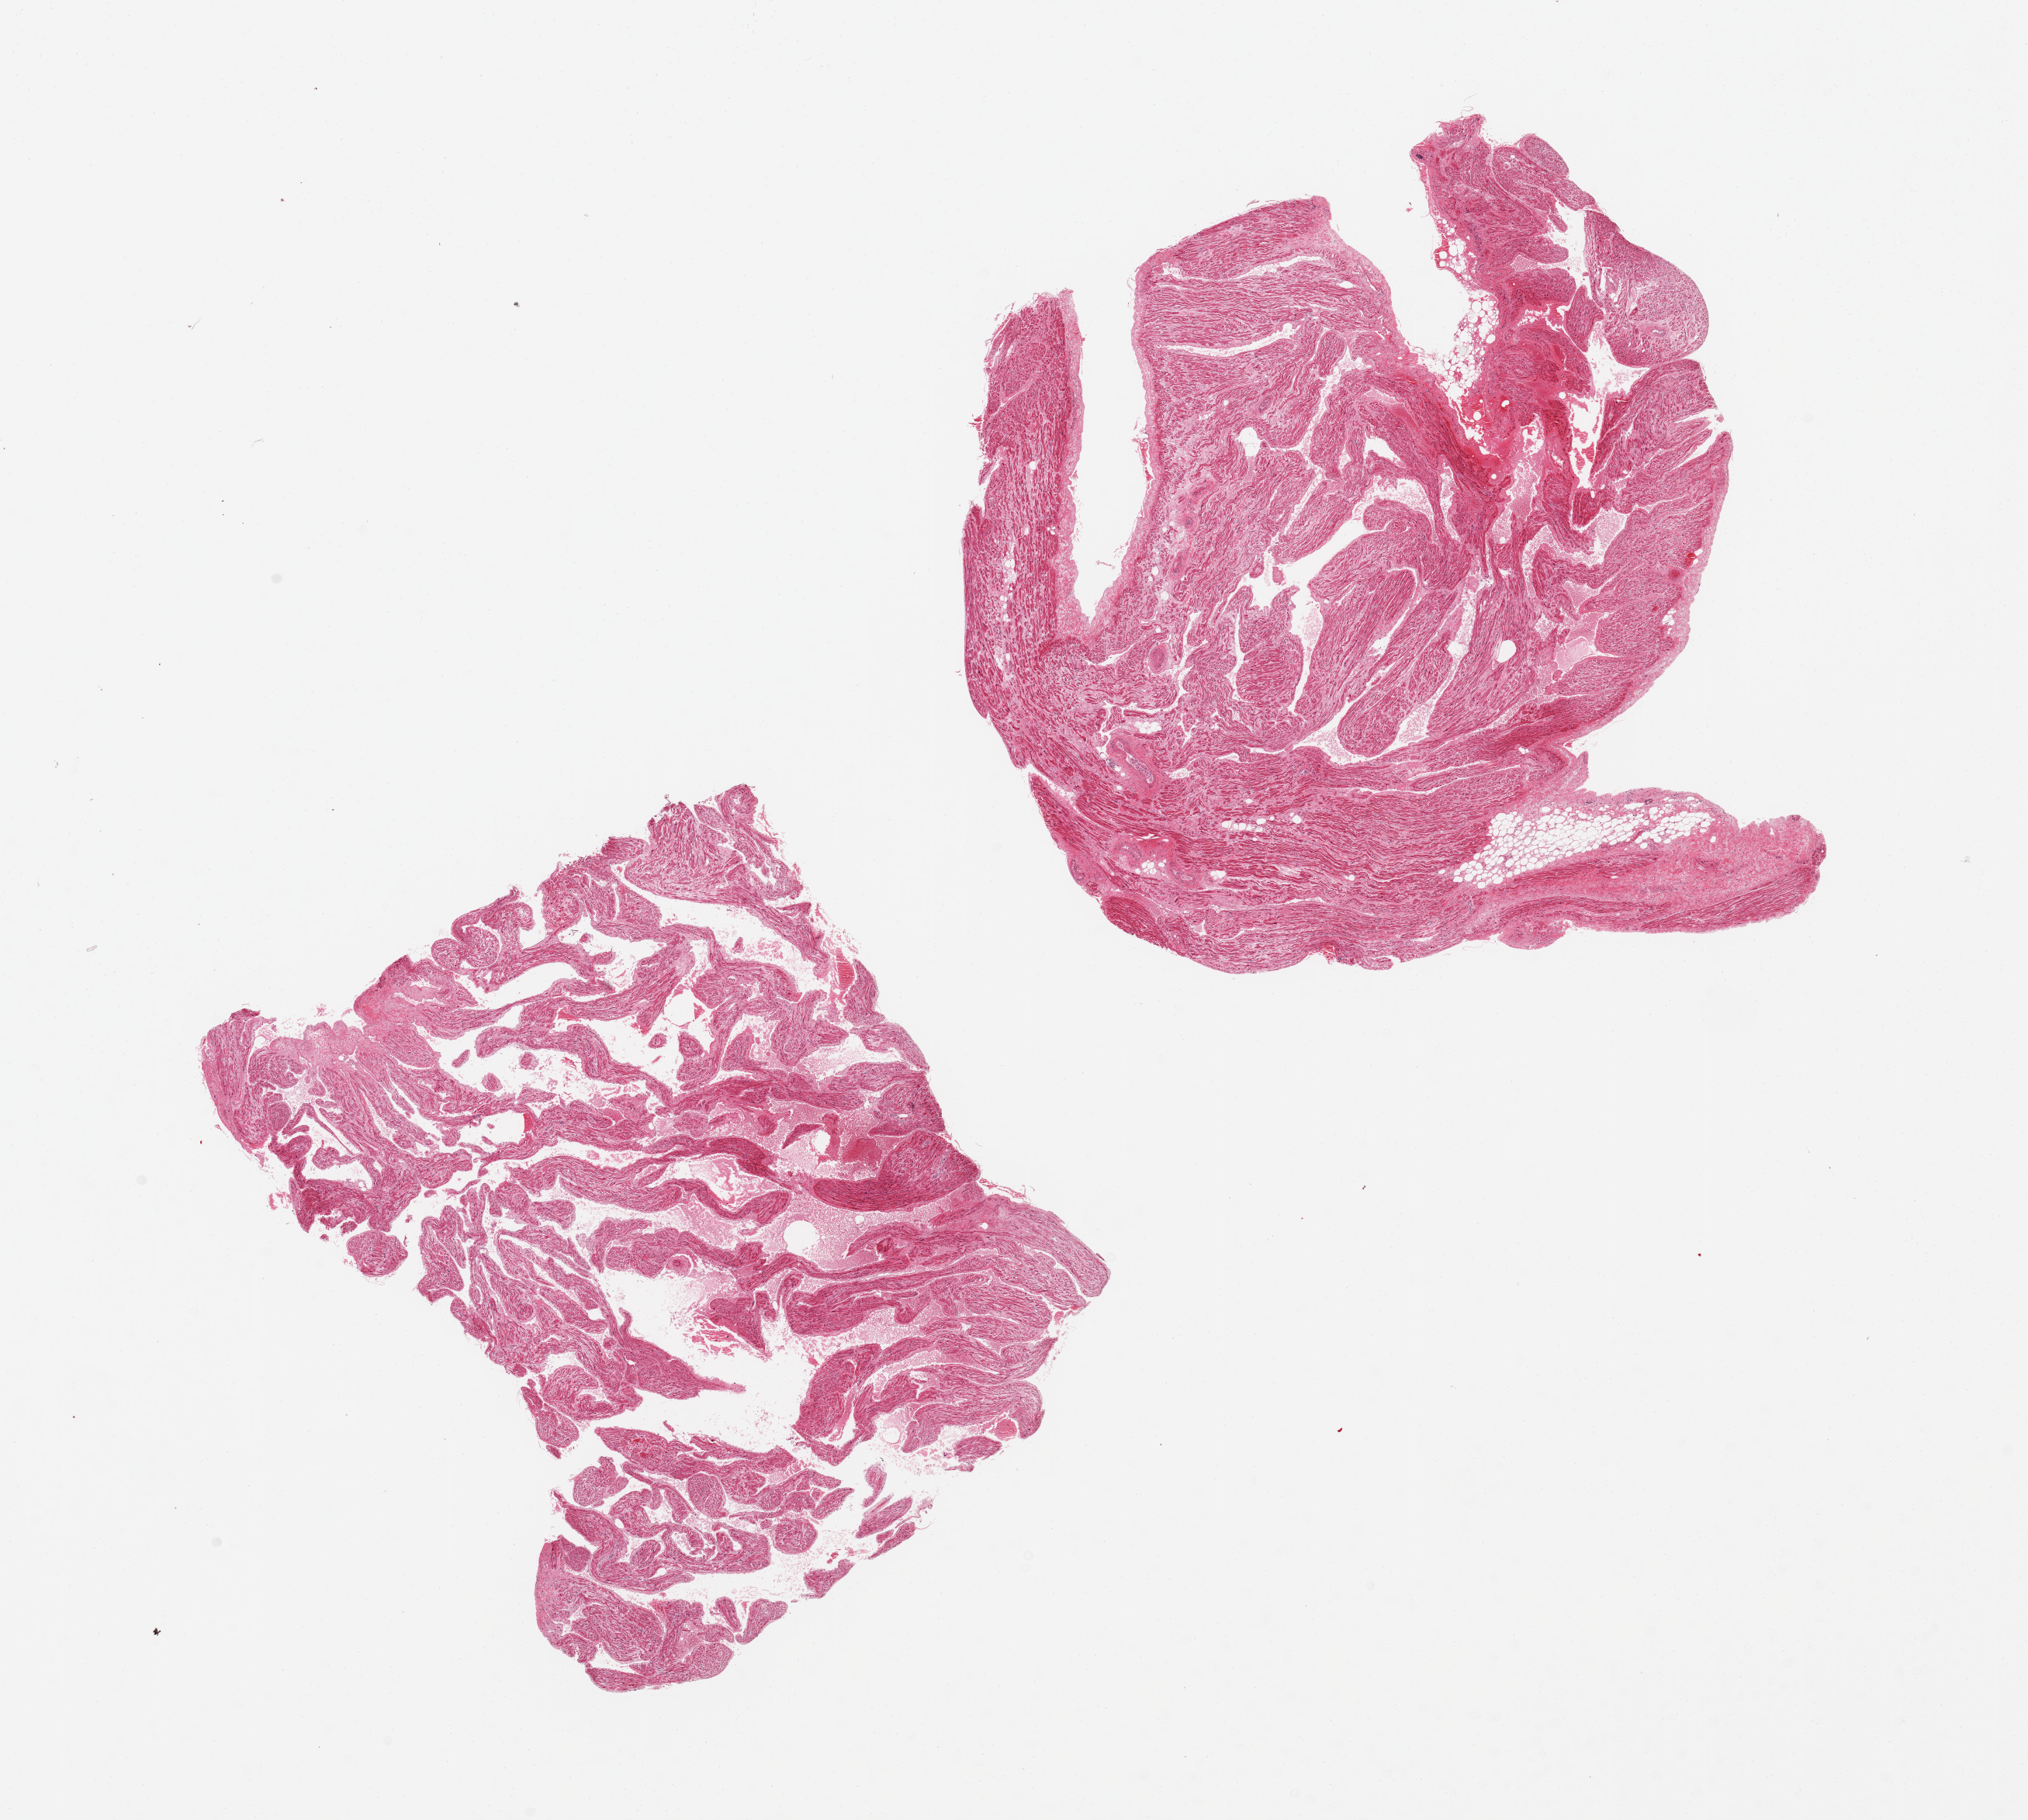
Haematoxylin and eosin whole-slide image, brightfield — a low-resolution overview of the entire scanned area, about 20.7 x 18.6 mm. PAXgene-fixed, paraffin-embedded tissue. Sampled site (target tissue): auricular appendage. Donor tissue sample. Donor sex: female.
* pathologist's review note for this sample: 2 pieces, moderate autolysis